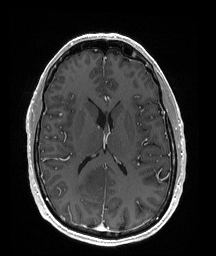
Brain MRI from a brain-tumour surgery series, one axial slice; position 84 of 176 along the scan axis; T1-weighted post-contrast; 1 mm slice thickness; 216 × 256 image matrix. From the clinical record (not read from this slice): histopathology: Oligodendroglioma; WHO grade: 2; IDH mutation: yes; tumour location: Right Parietal.
Structures marked on this image (outlined manually by an expert reader):
- tumour: bounding box <70,164,111,199> (left, top, right, bottom; pixels)